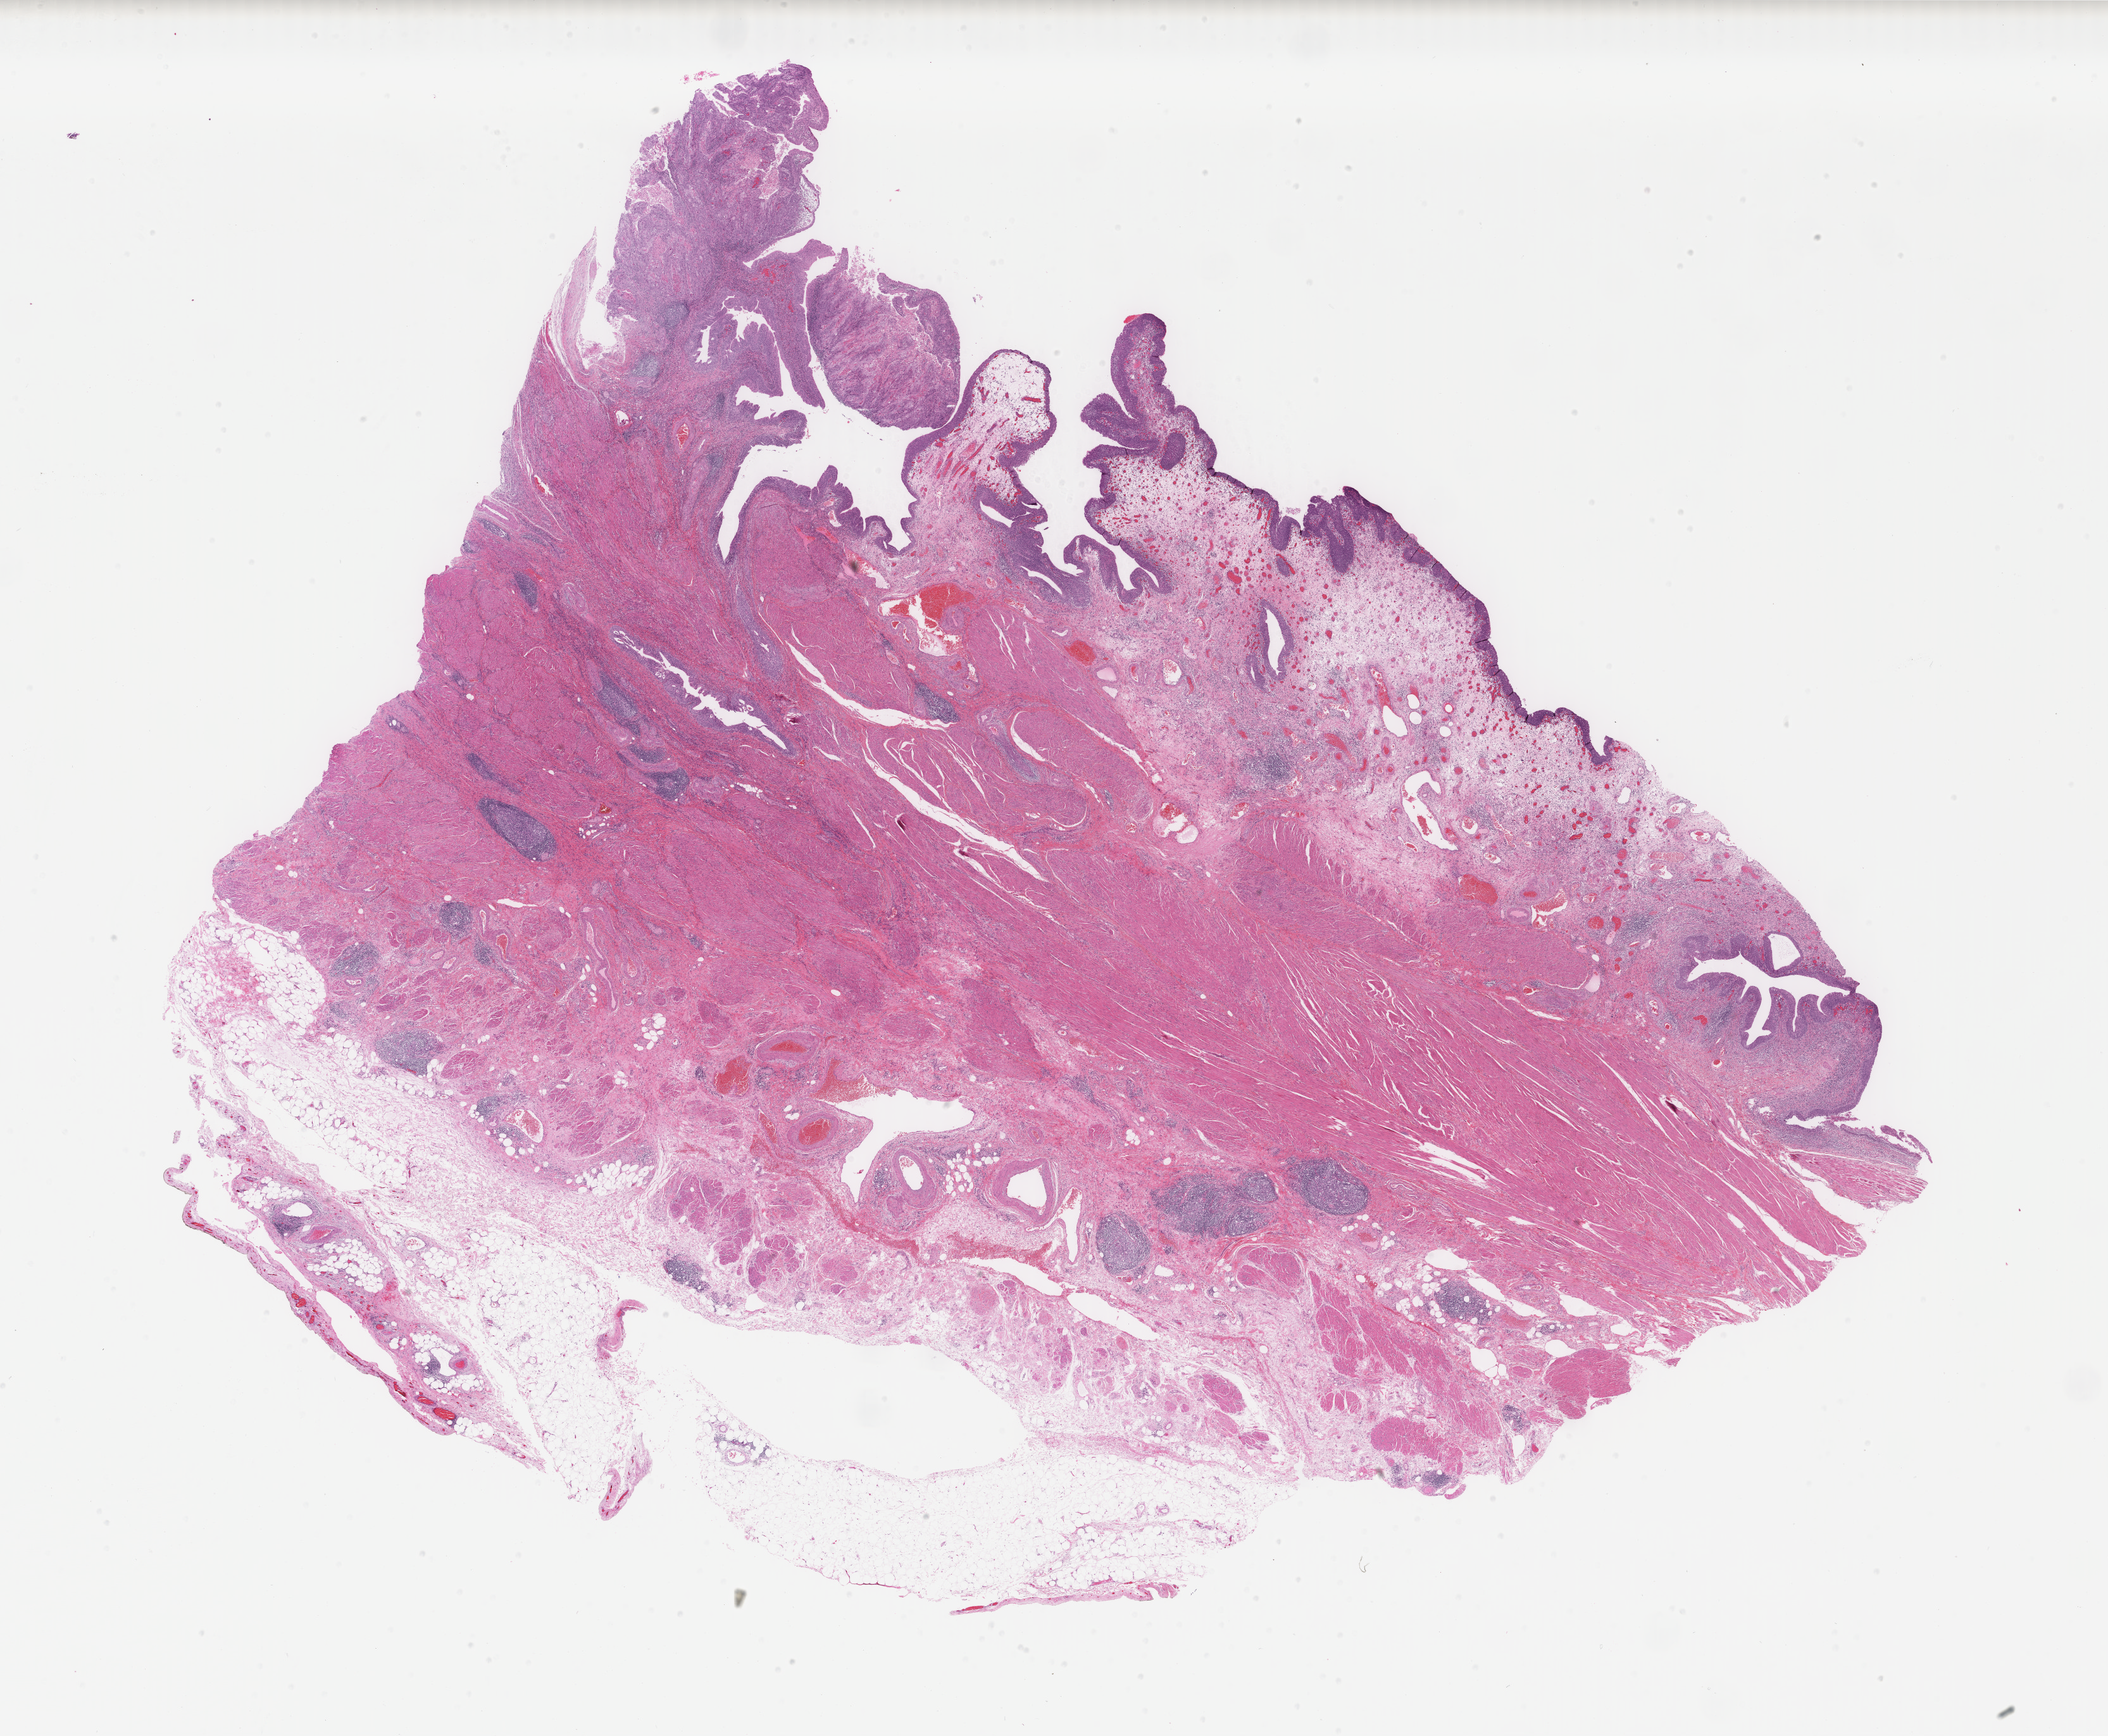
Hematoxylin and eosin (H&E) stained whole-slide image — a low-resolution overview of the entire scanned area, about 26.4 x 21.8 mm (acquisition: 40x scan). Formalin-fixed paraffin-embedded (FFPE) diagnostic section. Bladder, primary tumour sample. Patient: male, age at initial diagnosis 85 years. Histologic grade: high grade.
AJCC pathologic stage: II. Histologic diagnosis: Transitional cell carcinoma.